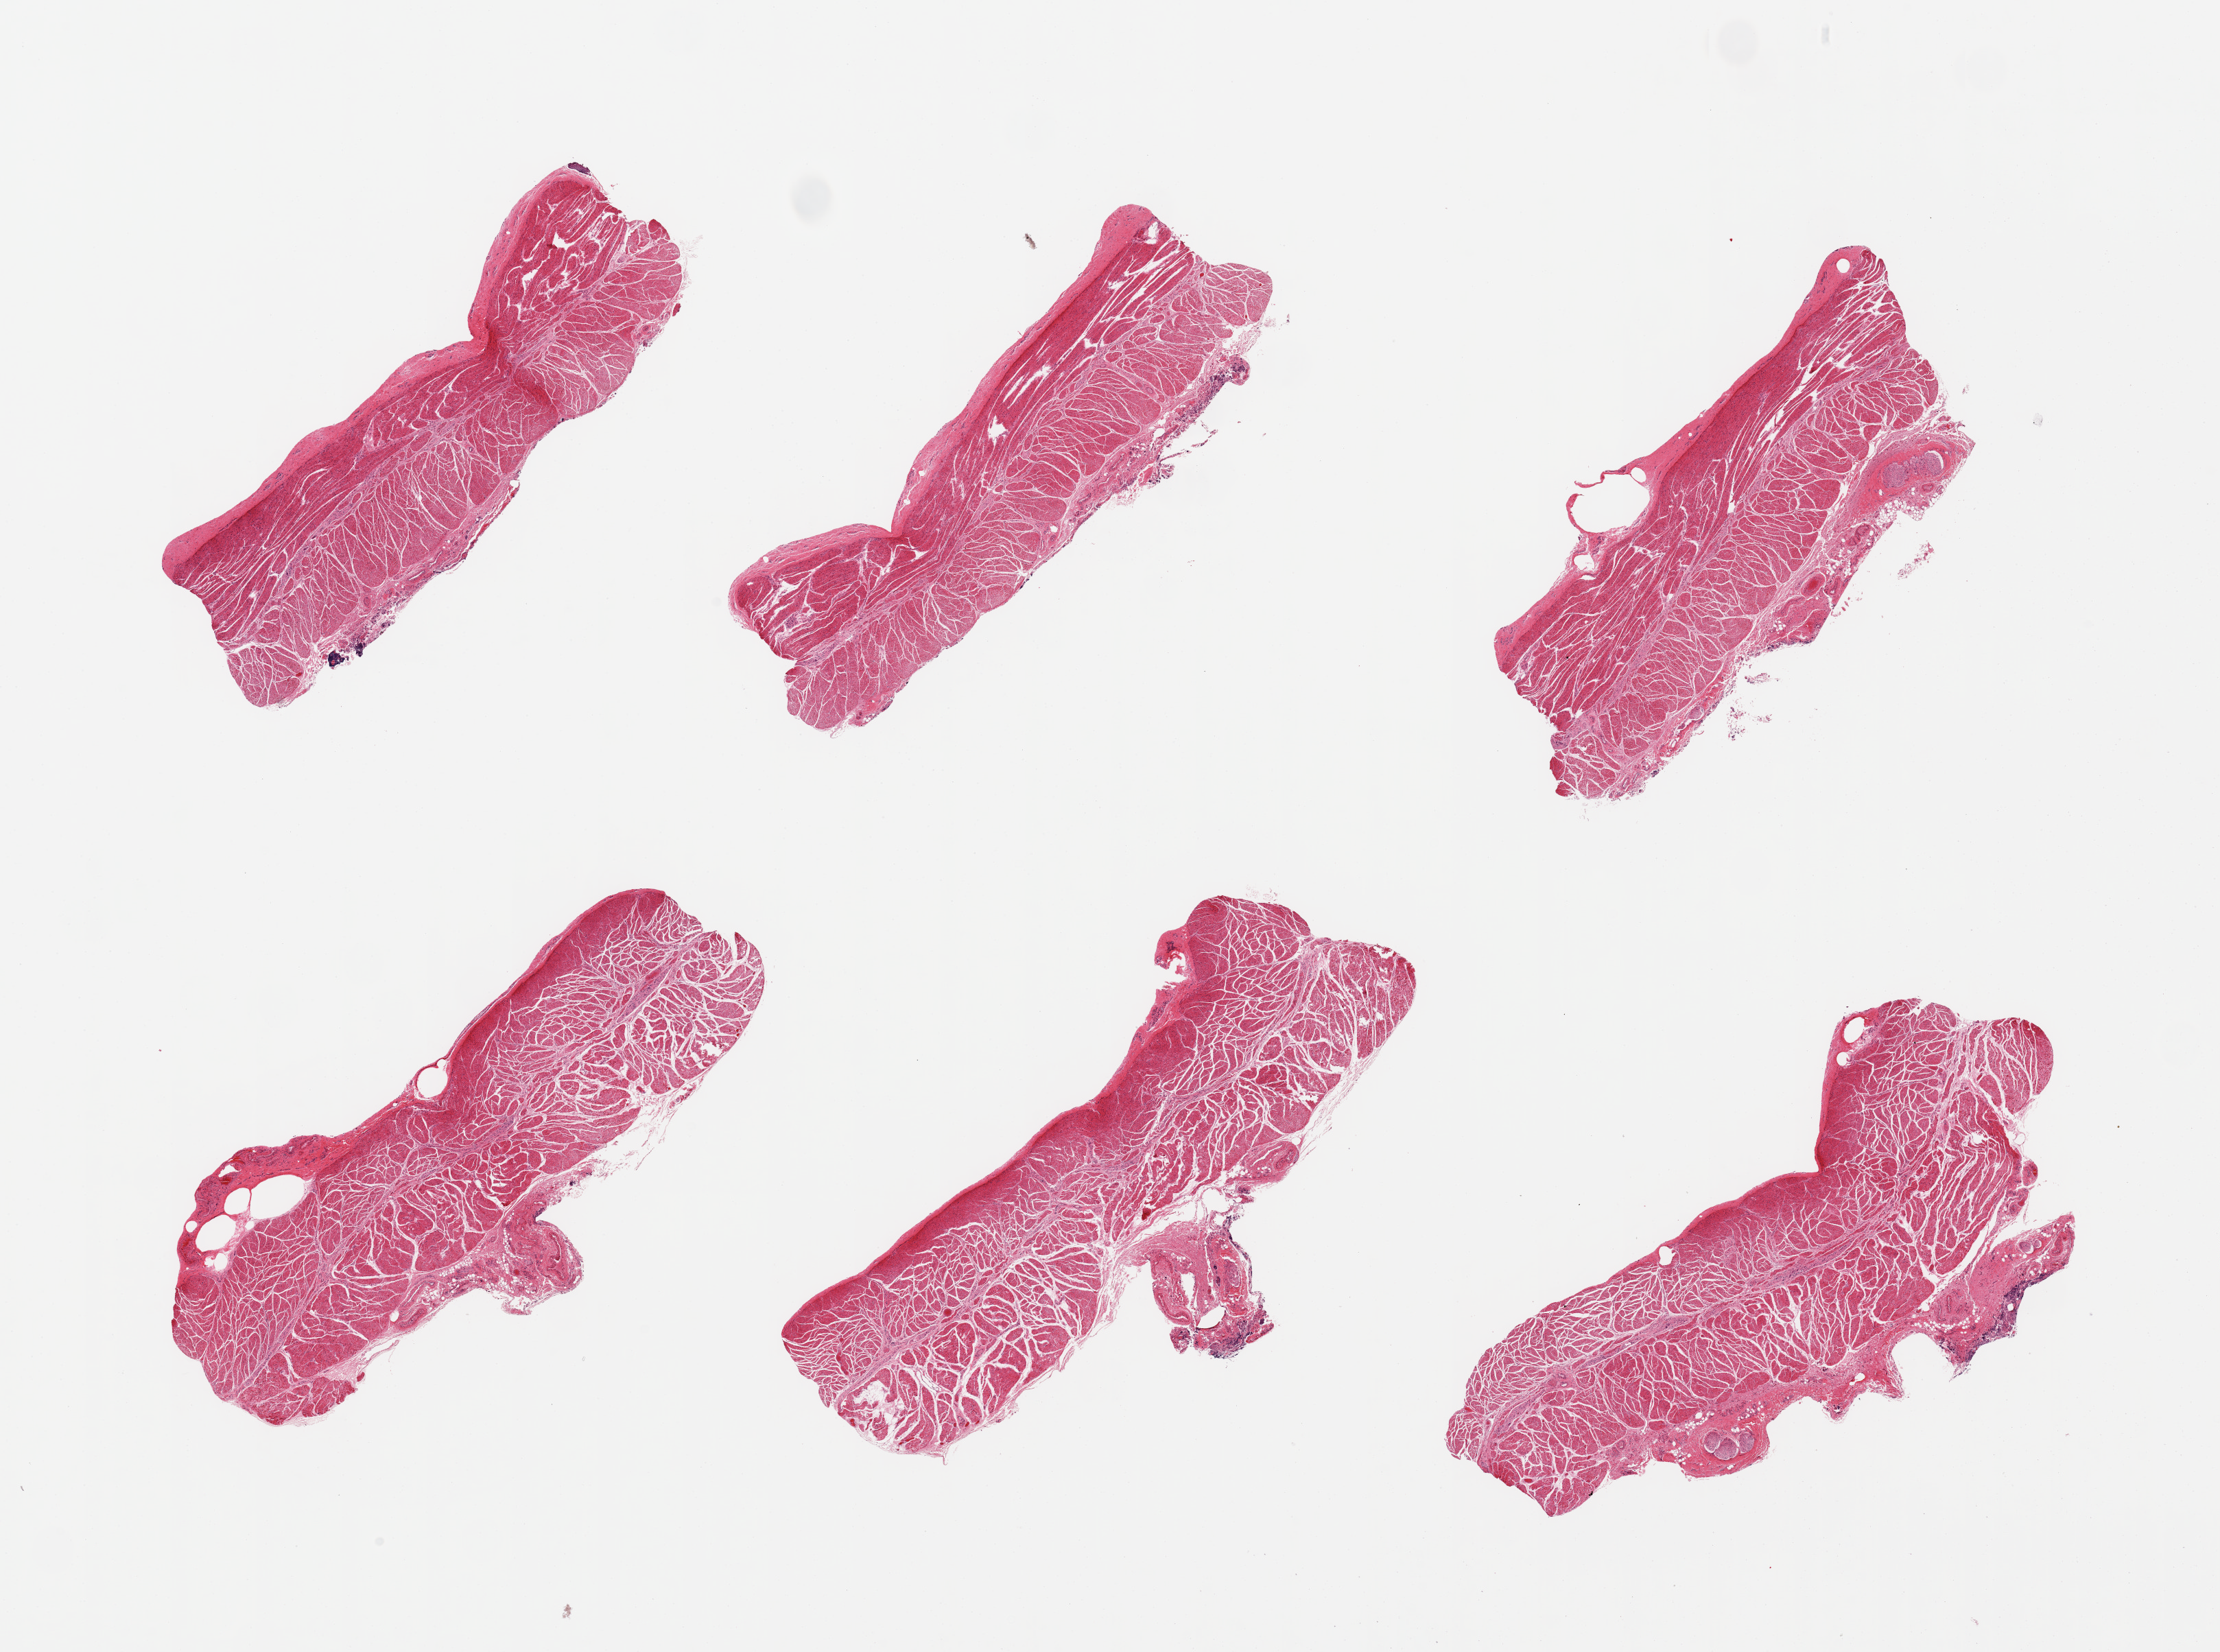
Whole-slide image, haematoxylin and eosin stain, shown as a low-resolution overview of the whole scanned area (about 25.6 x 19.0 mm, slide scanned at 20x); PAXgene-fixed, paraffin-embedded tissue; target tissue: esophageal muscle; donor tissue sample. Donor: female.
Review note (as recorded): 6 pieces; well trimmed.